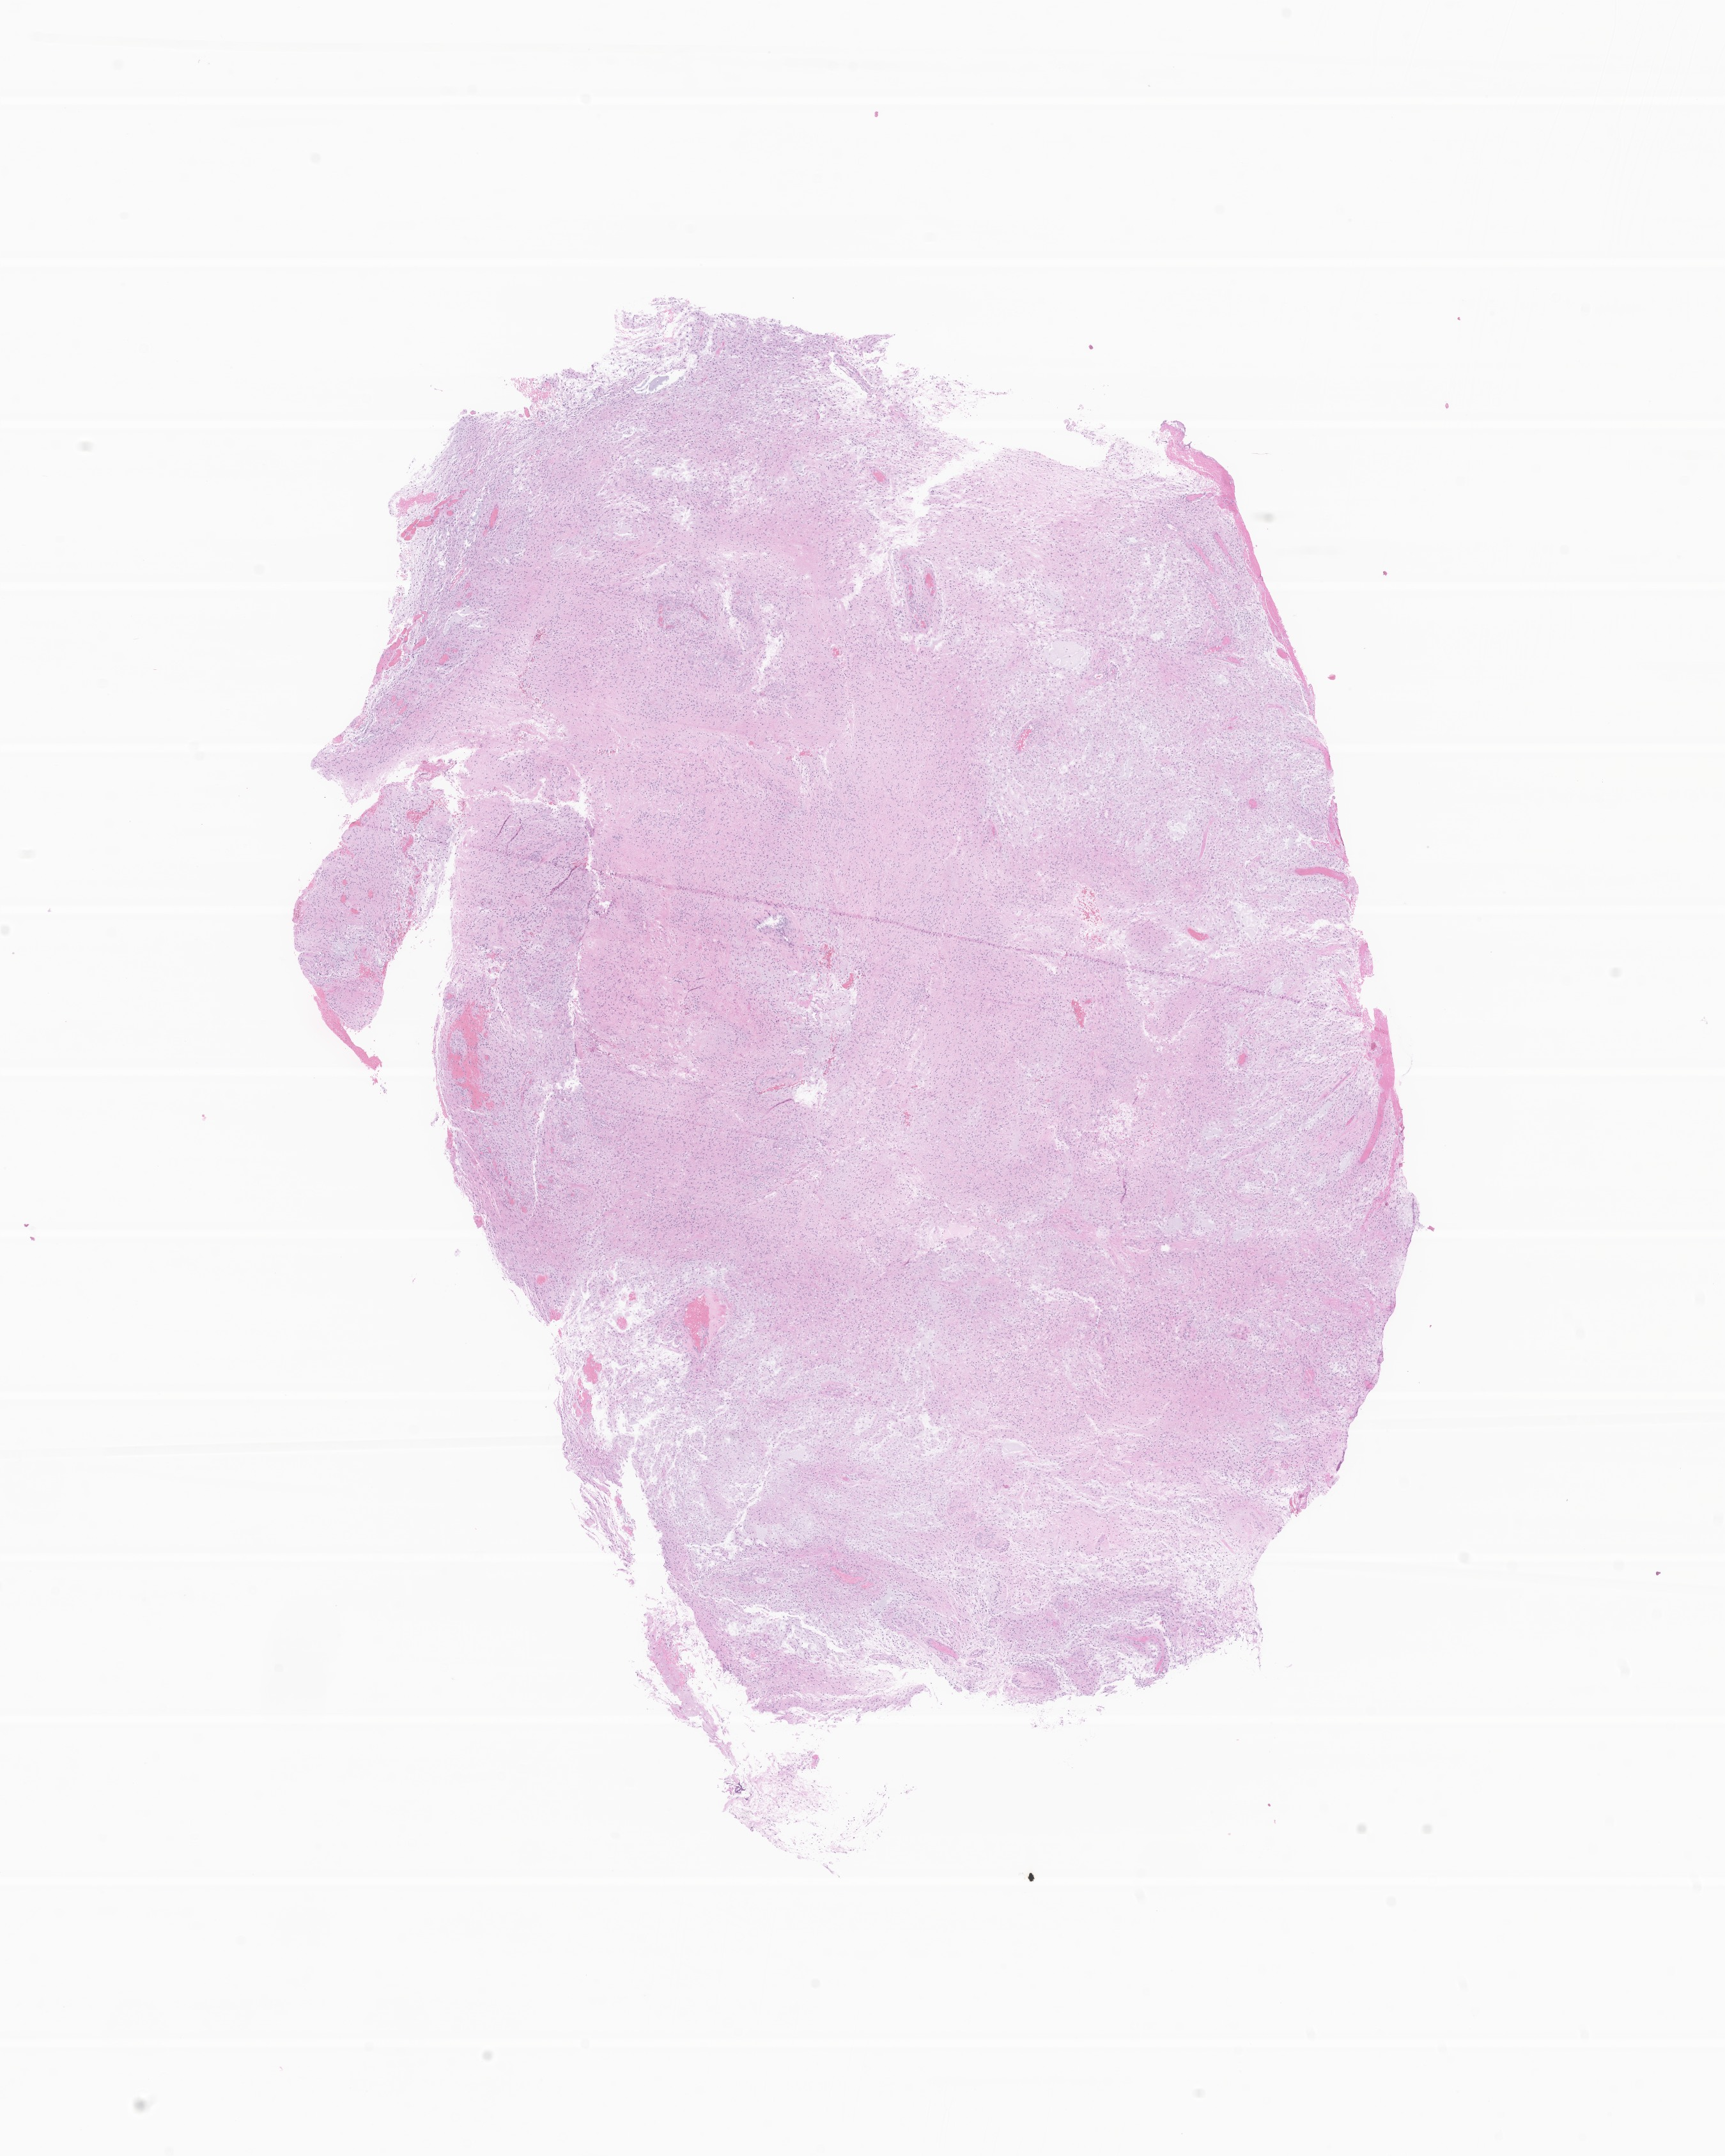
Digitized H&E-stained section of tumor tissue from the brain — low-resolution overview of the scanned area, about 11.4 x 14.2 mm. Formalin-fixed, paraffin-embedded (FFPE) tissue. Patient: female, age 69 months (5 years 9 months).
• recorded diagnosis: Glioma, malignant